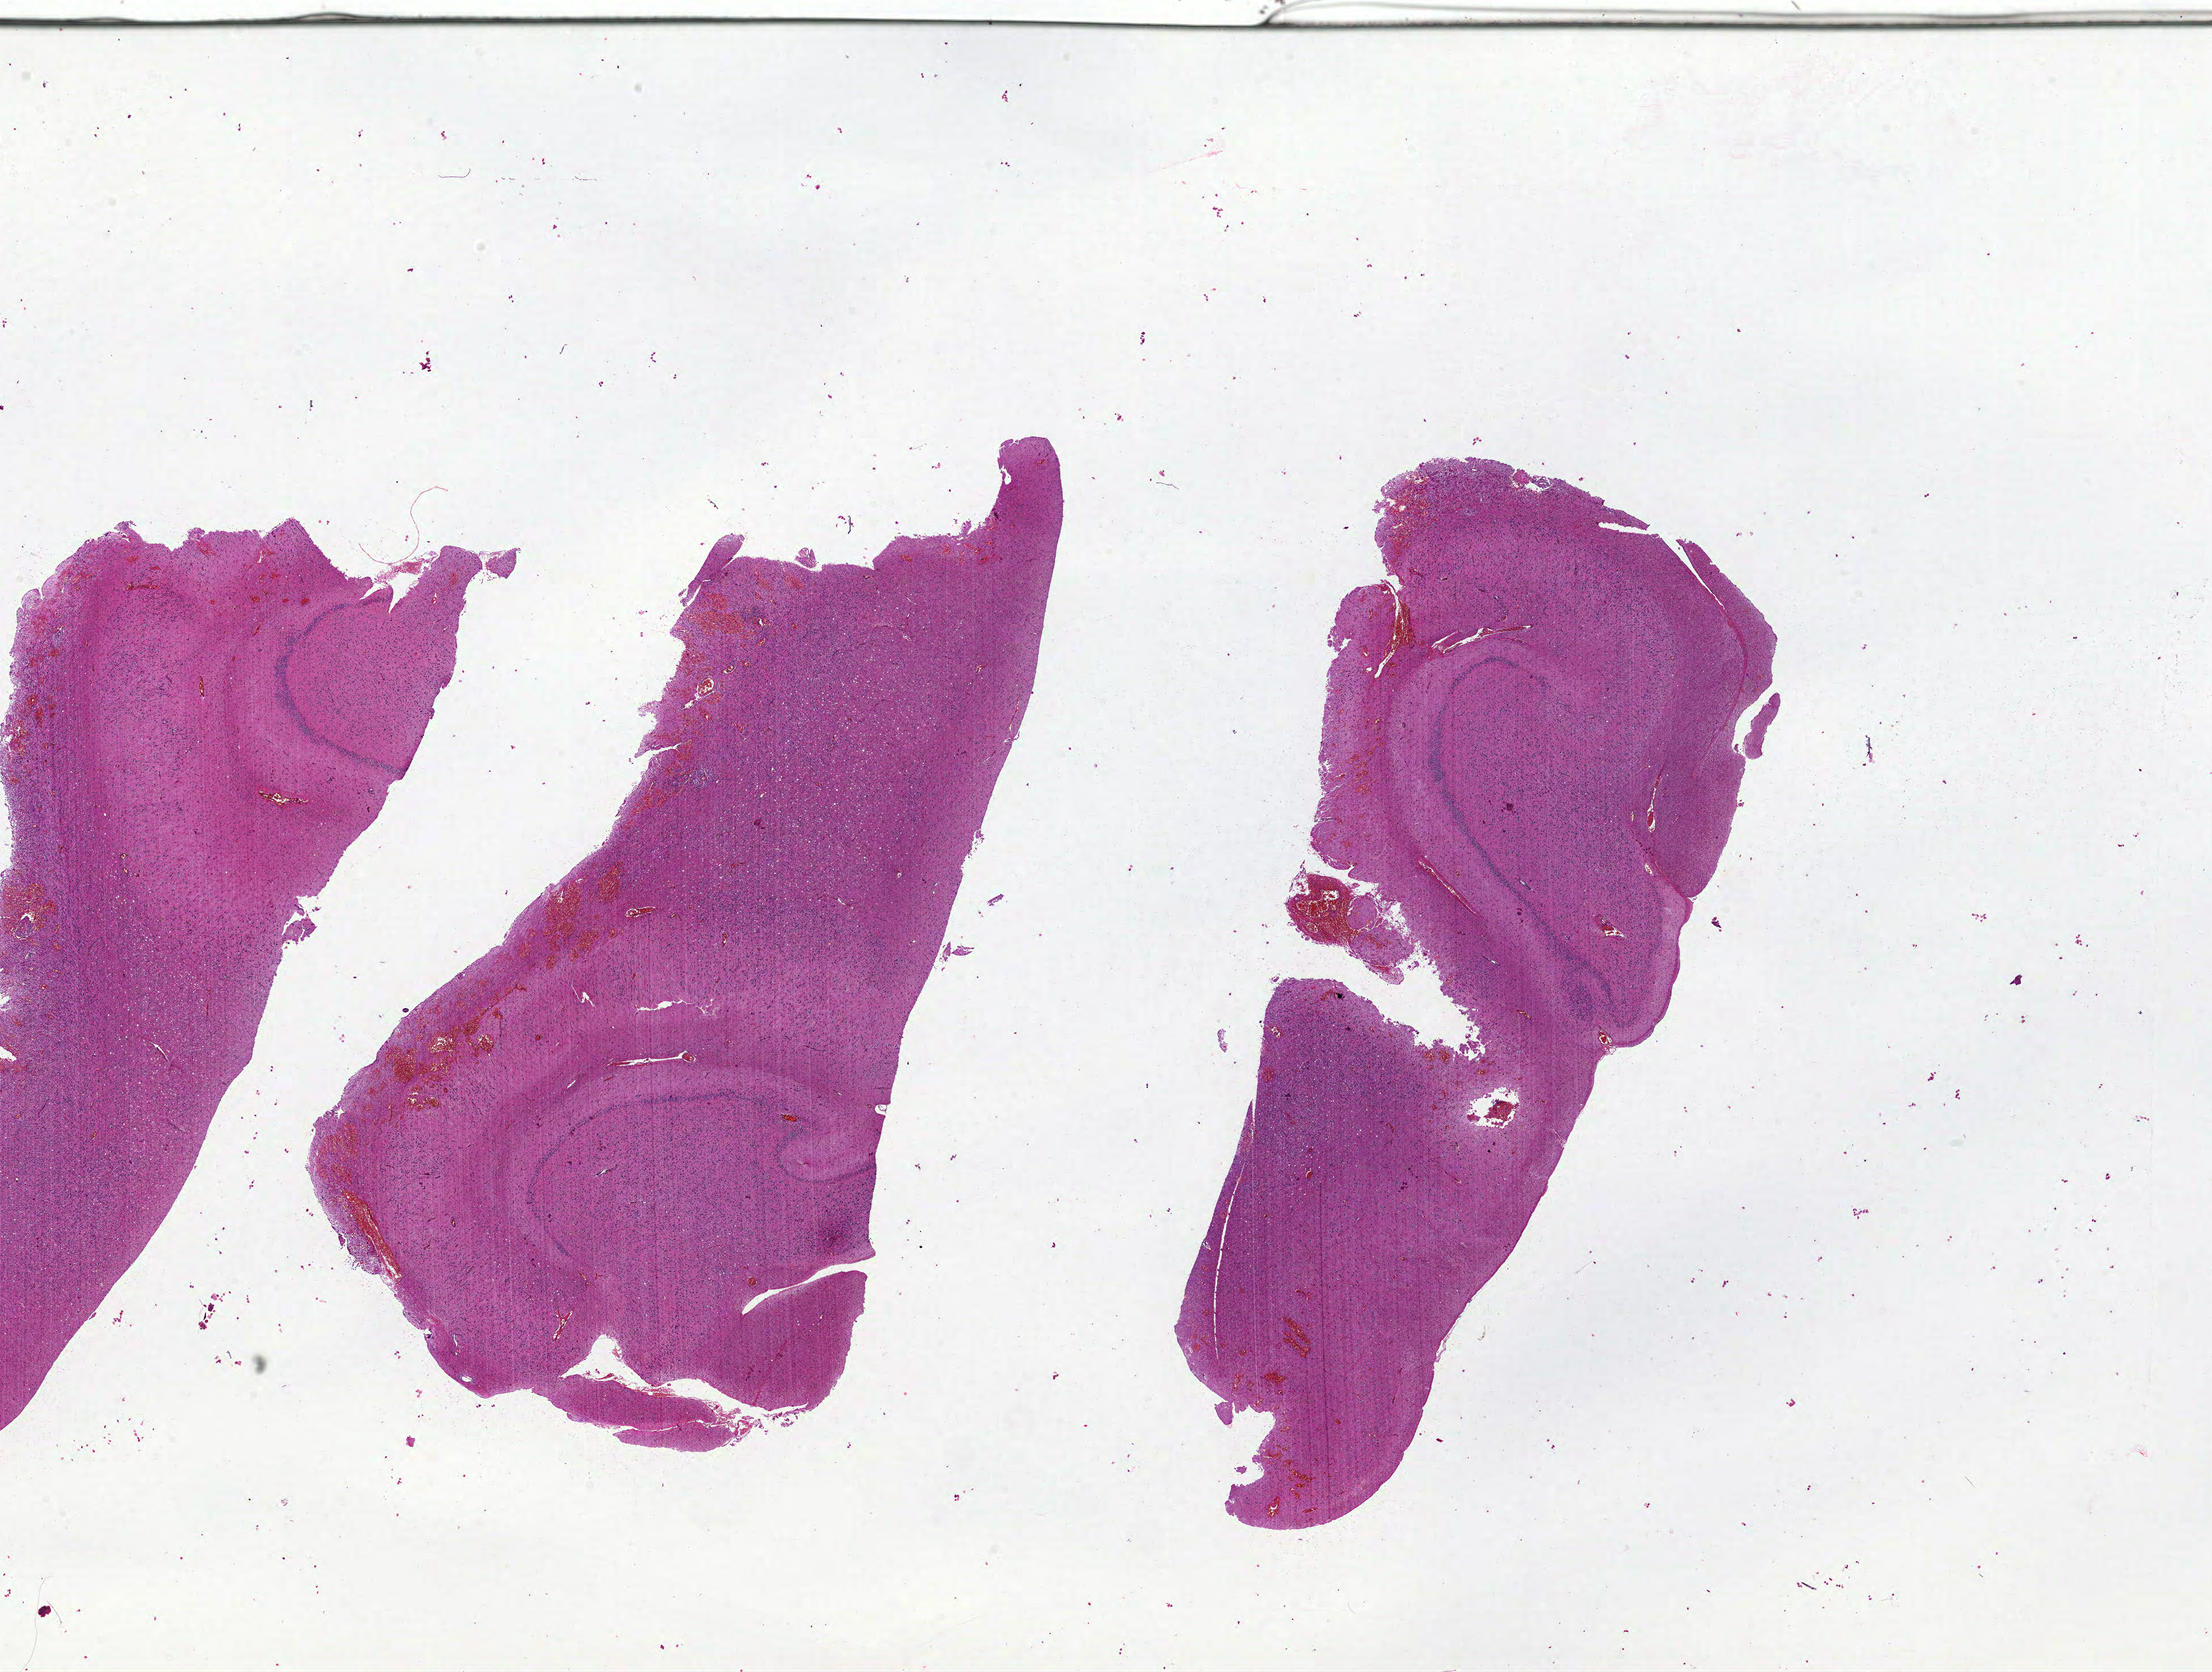
H&E-stained whole-slide image — low-resolution overview of the scanned area, about 31.0 x 23.4 mm (from a 20x scan), formalin-fixed paraffin-embedded (FFPE) diagnostic section, brain, primary tumour sample. Male, age 46 years at initial diagnosis.
Histologic diagnosis: Glioblastoma.